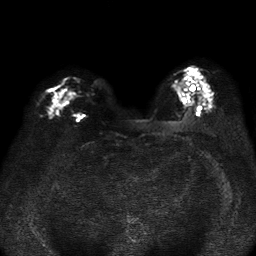
Breast MRI, one axial slice. Position 21 of 37 along the scan axis. Diffusion-weighted series; image 2 of 4 stored at this slice position (different b-values; order by instance number). 1.5 T. 256 × 256 image matrix, field of view 320 × 320 mm. Female patient.
Structures marked on this image (manually delineated by an expert):
- tumour on diffusion-weighted imaging: bounding box (x1, y1, x2, y2) in pixels: (67, 88, 73, 98)